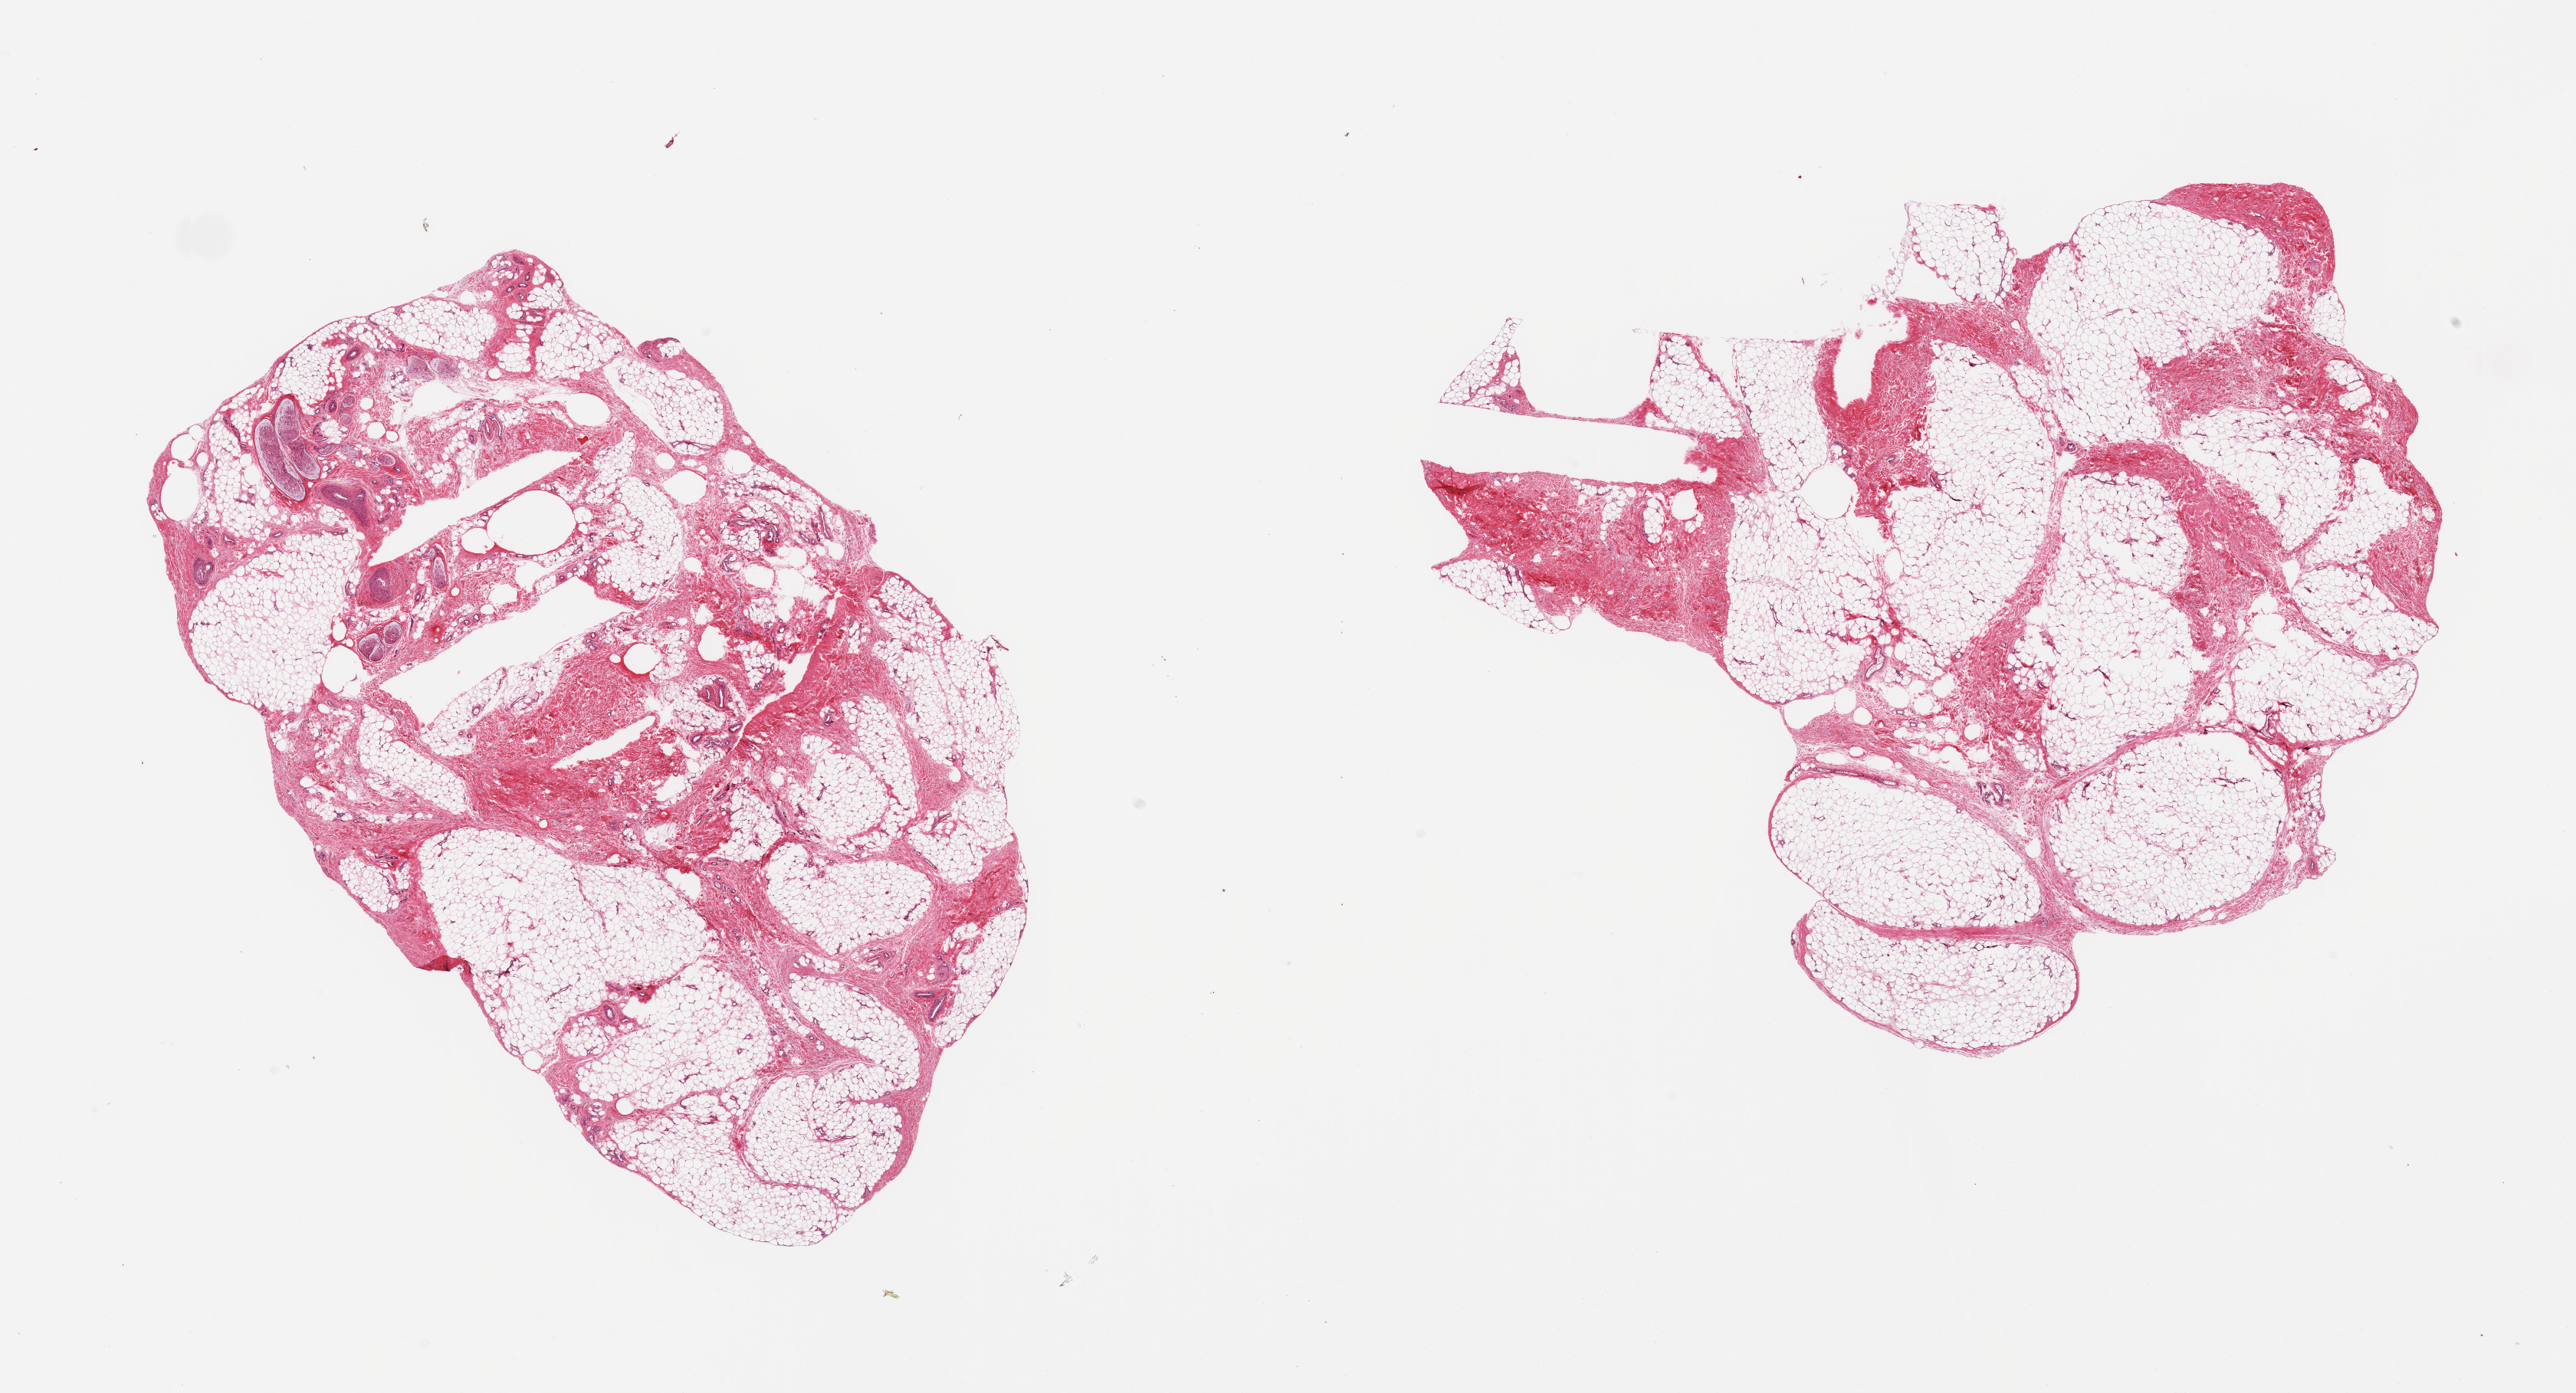
Hematoxylin and eosin (H&E) whole-slide image, low-resolution overview of the scanned area, about 26.6 x 14.4 mm; PAXgene-fixed, paraffin-embedded tissue; sampled site (target tissue): adipose tissue; donor tissue sample. Donor: male.
Review note (as recorded): 2 pieces; lobulated mature adipose tissue; ~30% fibrous septa with vessels and nerves.